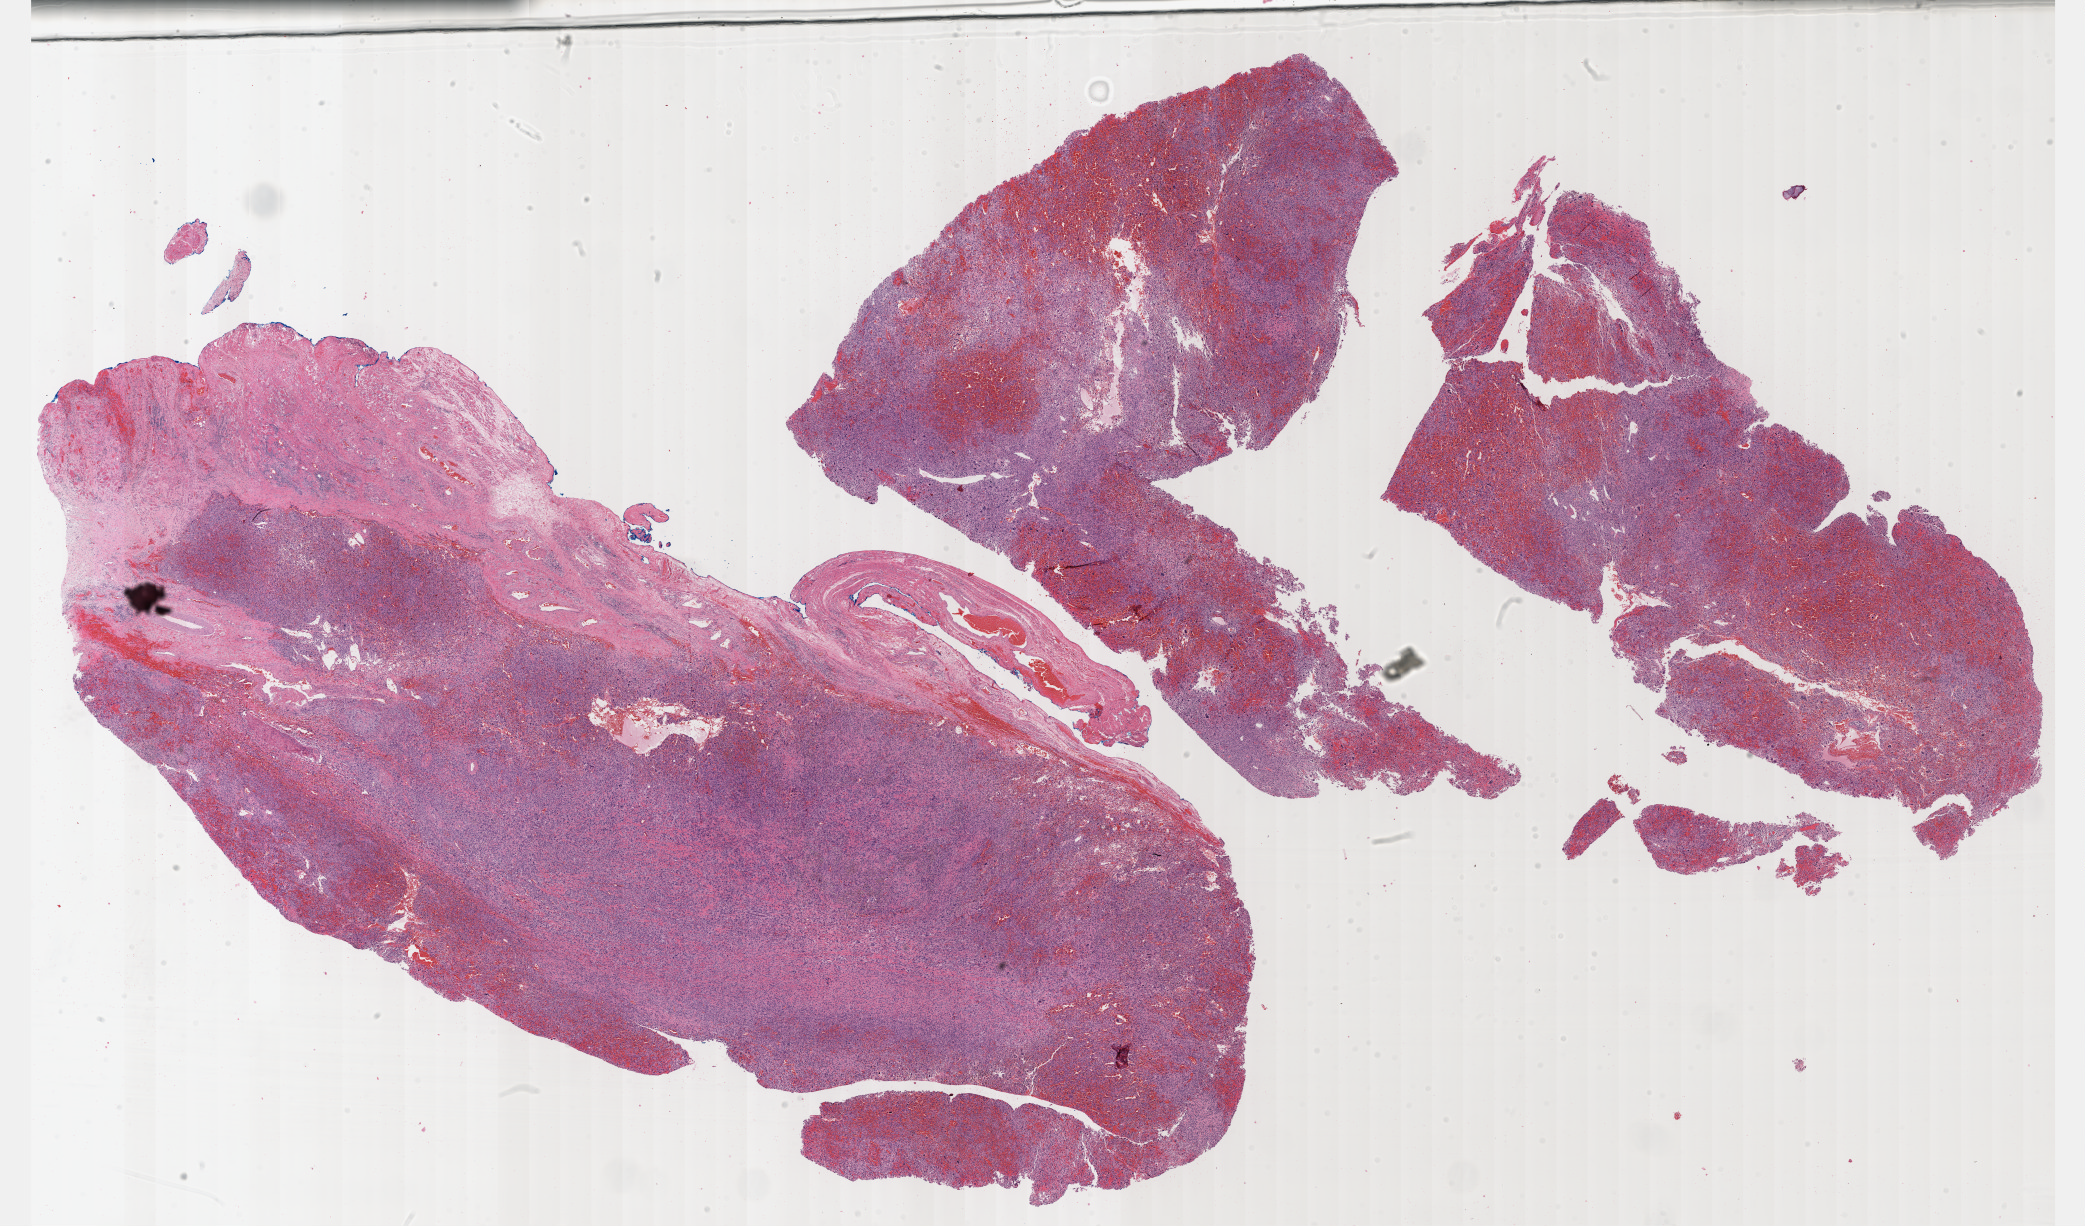
Whole-slide histology image, H&E — low-resolution overview of the scanned area, about 33.7 x 19.8 mm (from a 40x scan); formalin-fixed paraffin-embedded (FFPE) diagnostic section; sample: primary tumour, connective, subcutaneous and other soft tissues. Male patient; age at initial diagnosis 56 years.
Pathologic diagnosis: Undifferentiated sarcoma (connective, subcutaneous and other soft tissues of lower limb and hip).